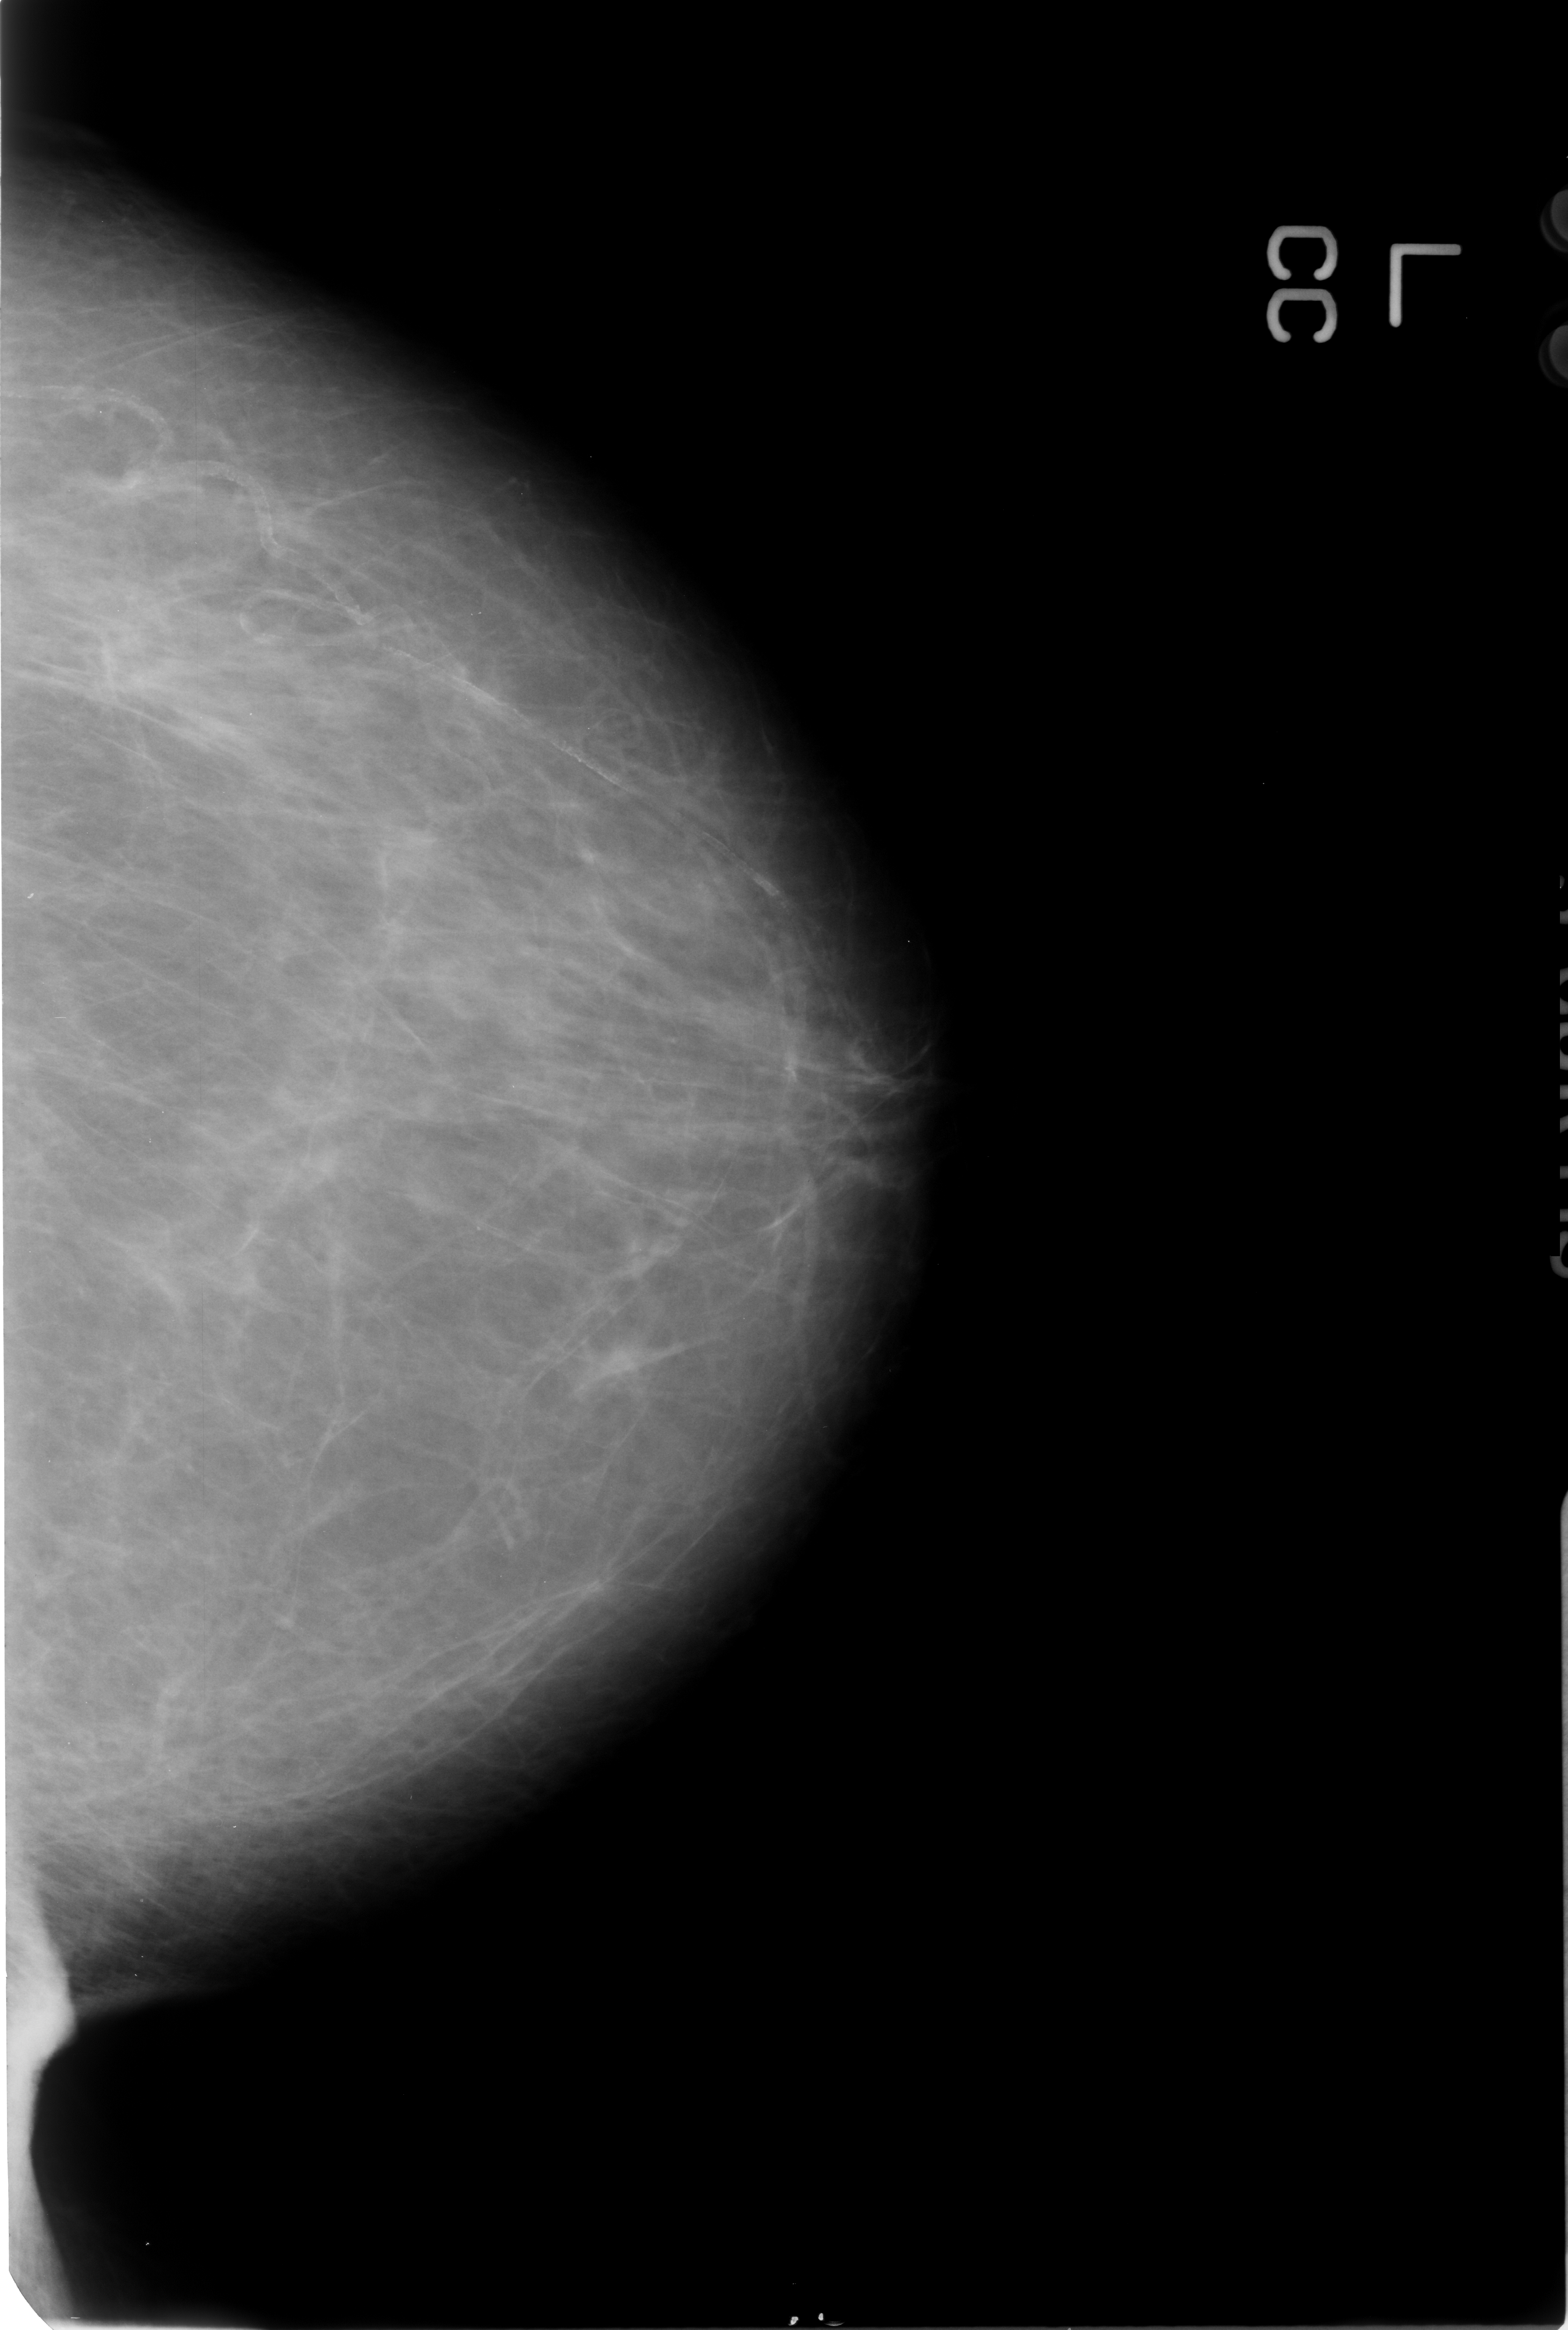
Digitized screen-film mammogram; left breast; CC view; breast composition: scattered fibroglandular densities (BI-RADS density category 2 of 4).
- Radiologist-marked abnormalities on this image: calcifications, morphology vascular; BI-RADS assessment category 2; subtlety rating 3 on a 1 (subtle) to 5 (obvious) scale; benign; no additional work-up was recommended (benign without callback).